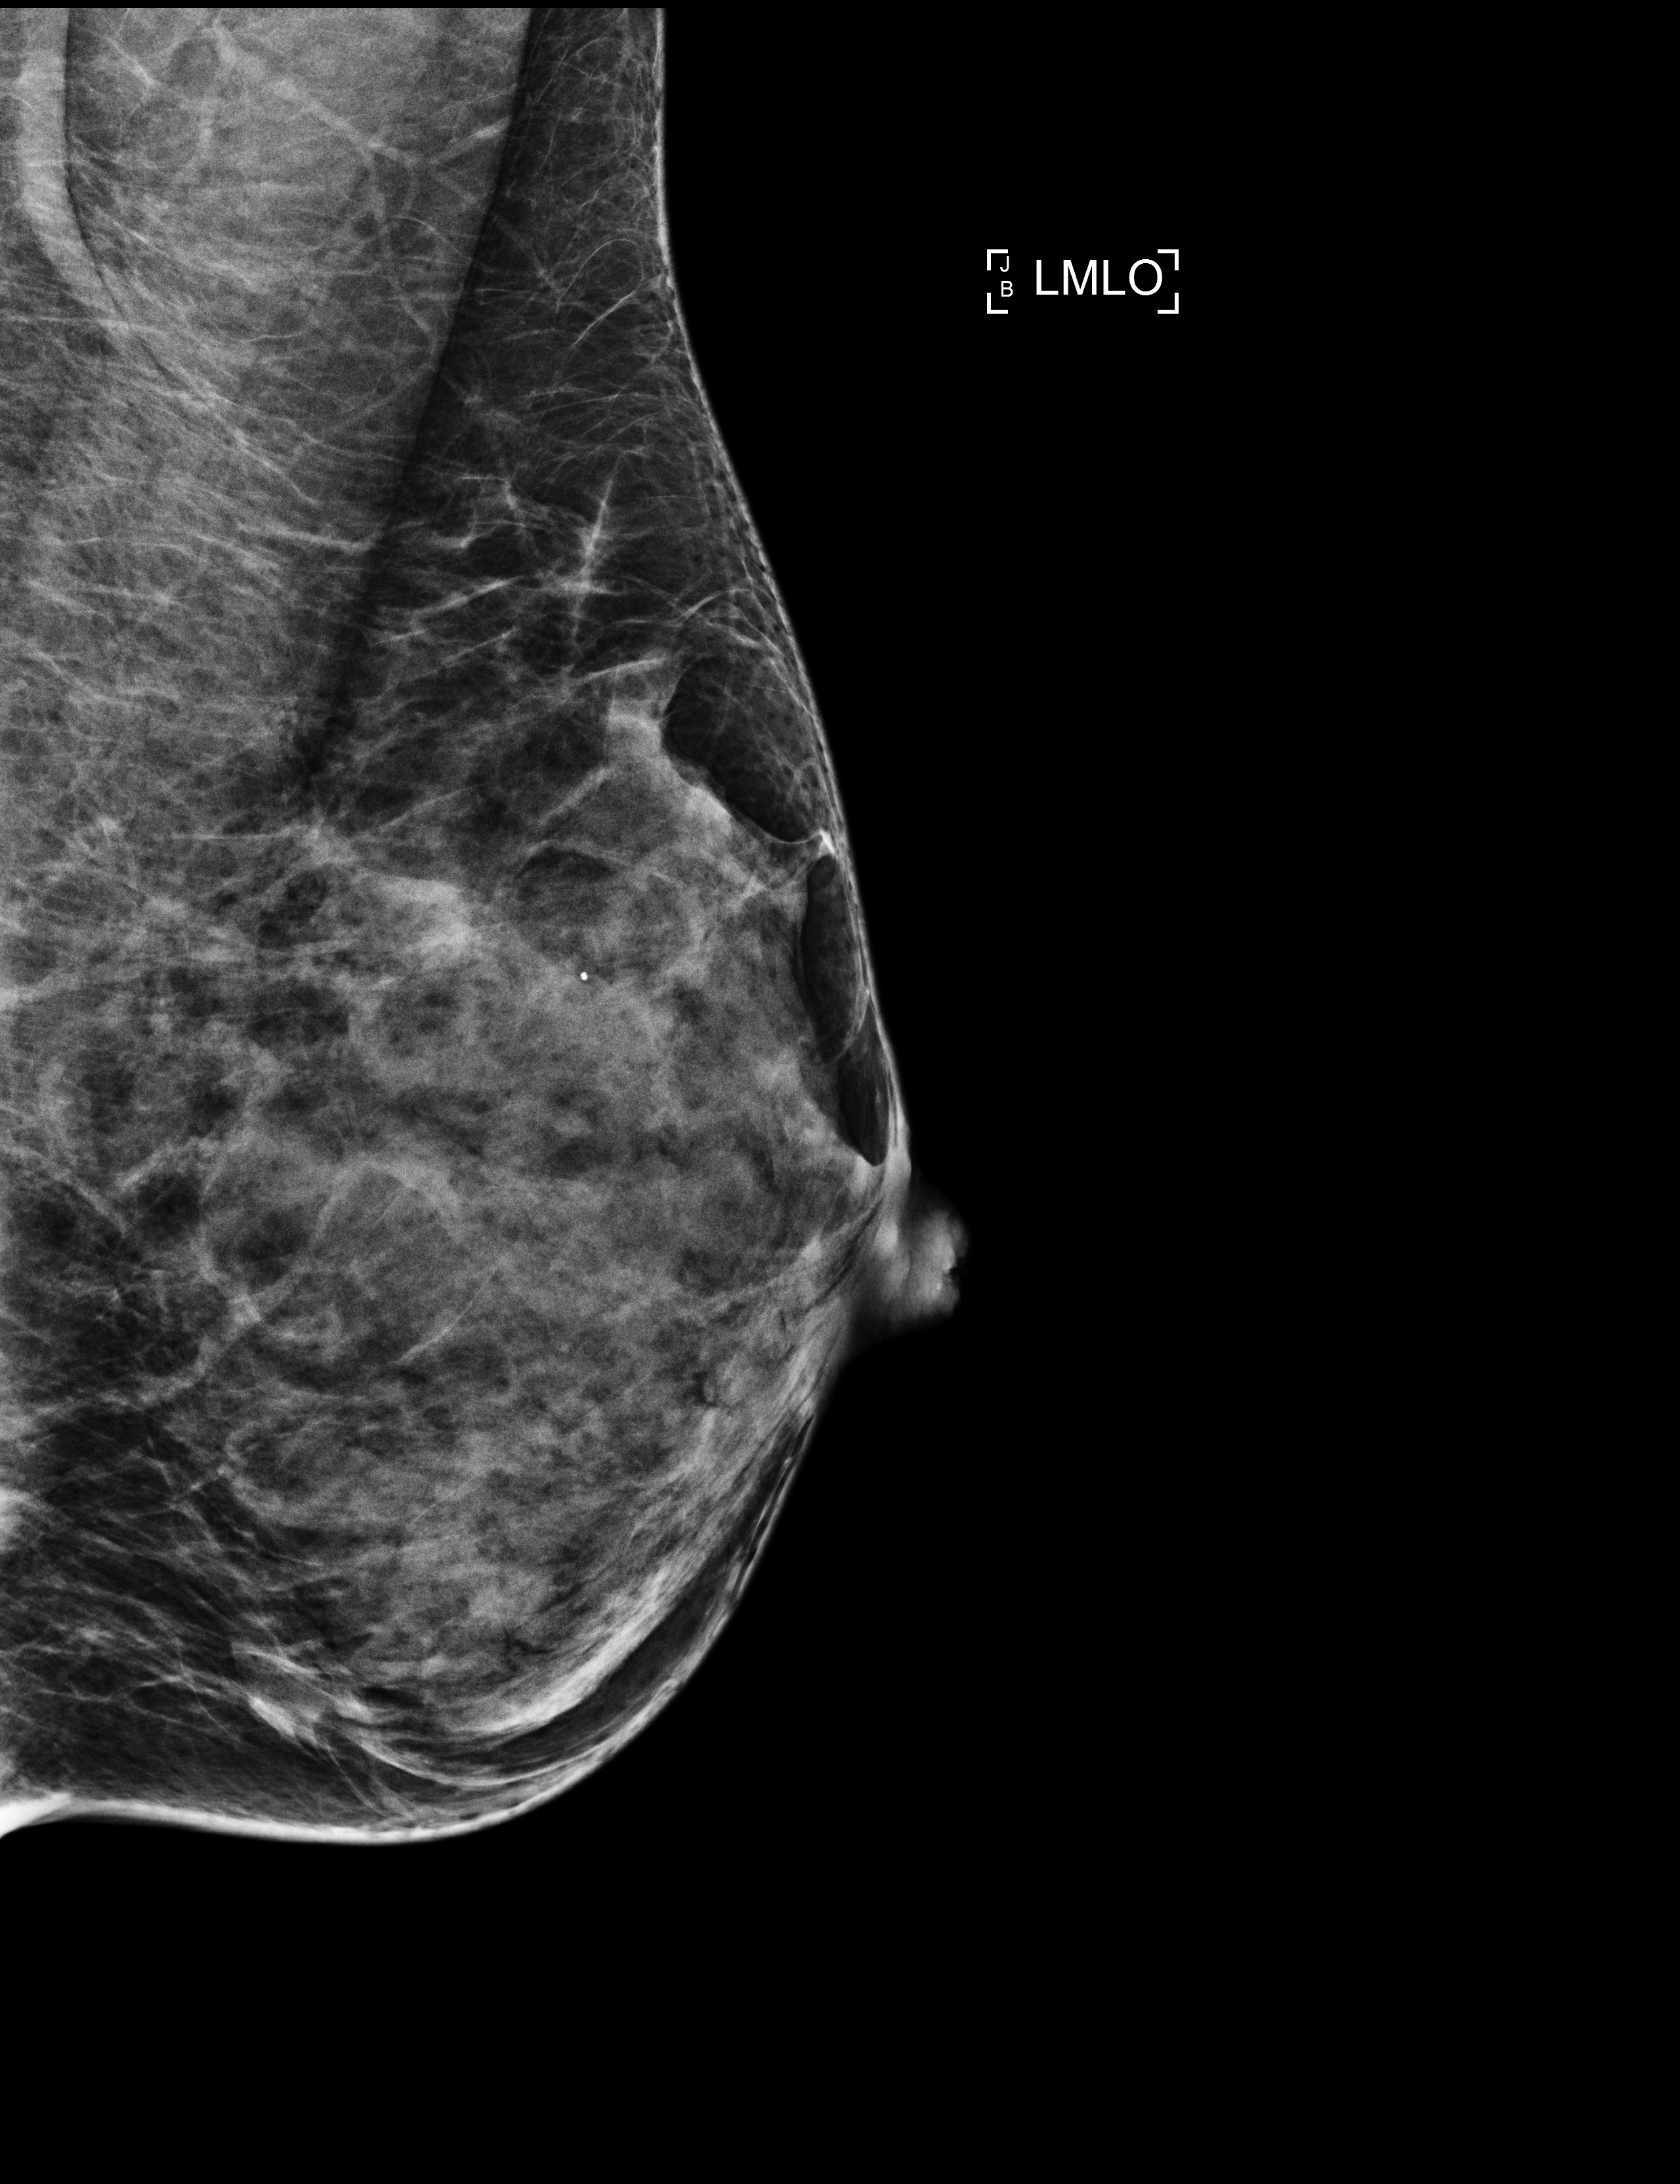
Screening examination, compressed breast thickness 41 mm. Female patient, age 47 years.
Image type: full-field digital mammogram. Breast: left. Projection: MLO view.